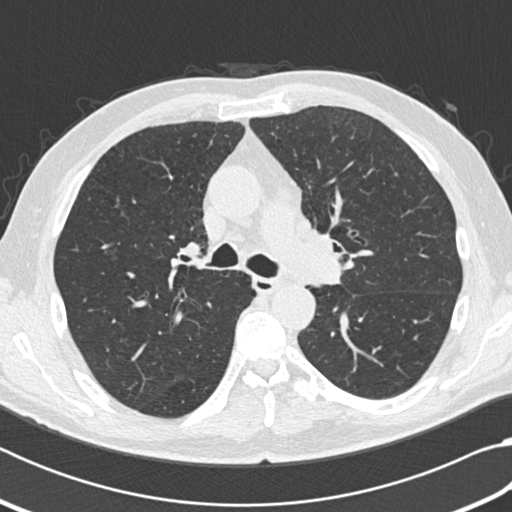
Chest CT (low-dose screening protocol), one axial image; third annual screen; lung window (W 1500 / L -600 HU); 2 mm slice thickness; standard (soft-tissue) reconstruction kernel (B30f); slice 75 of 207 in the series; 512 × 512 image matrix. Male participant, aged 64 years at enrolment. Current smoker at enrolment.
- Expert reader's lesion annotation, bounding box [x1, y1, x2, y2] px = [252, 174, 305, 221].
- No non-calcified nodule or mass ≥4 mm was recorded by the screening reader at this exam.
- Participant outcome: lung cancer diagnosed 163 days after this screen — small cell carcinoma, NOS, mediastinum, stage IV (AJCC 6th edition).